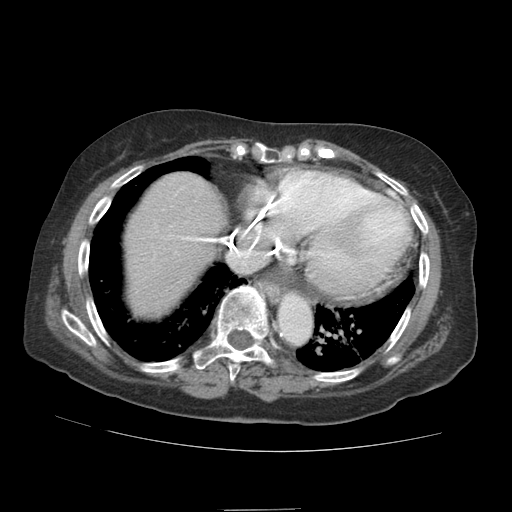
Contrast-enhanced abdominal CT (liver protocol), one axial slice; position 79 of 89 along the scan axis; reconstruction kernel STANDARD; soft-tissue window (W 400 / L 40 HU); 512 × 512 image matrix, field of view 360 × 360 mm. From the clinical record (not read from this slice): diagnosis: hepatocellular carcinoma (patient treated with transarterial chemoembolisation; whether this scan precedes or follows treatment is not stated here); TNM stage (as recorded): Stage-II.
Structures marked on this image (semi-automatic segmentation, software-assisted and operator-edited):
- abdominal aorta: bounding box <278,296,310,340> (left, top, right, bottom; pixels)
- liver parenchyma outside the tumour (the mass and vessels are separate outlines, so this box may not span the whole liver): <124,172,226,314>
- liver vessels: <181,236,215,242>